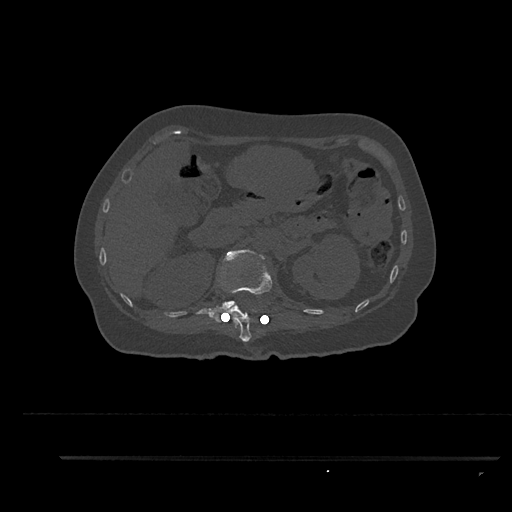
CT including the spine, one axial slice. 120 kVp. Bone window (W 1800 / L 400 HU). 0.5 mm slice thickness. 512 × 512 image matrix, field of view 408 × 408 mm. Female patient, age 44 years. Case-level facts recorded for this patient, not image findings: primary cancer: renal.
Structures marked on this image (semi-automatic segmentation, software-assisted and operator-edited):
- L1 vertebra: bounding box (x1, y1, x2, y2) in pixels: (209, 249, 265, 318)
- T12 vertebra: (210, 251, 273, 342)